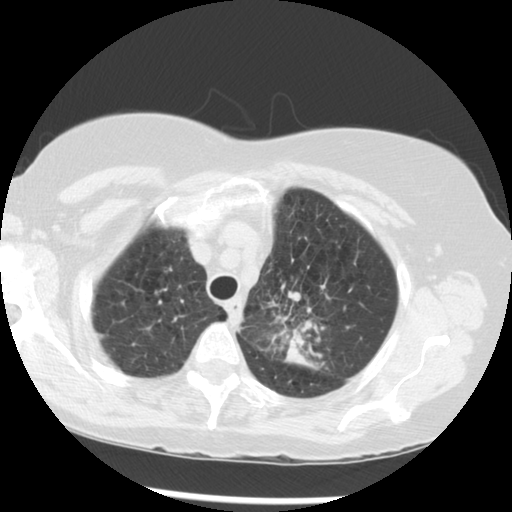
Axial slice from a low-dose chest CT screening exam. Third screening round (two years after baseline). Lung window (W 1500 / L -600 HU). 2.5 mm slice thickness. Standard (soft-tissue) reconstruction kernel (STANDARD). Slice 231 of 283 in the series. 512 × 512 image matrix. Female participant, aged 70 years at enrolment. Current smoker at enrolment.
• Lesion marked by an expert reader, bounding box <255,281,352,369> (left, top, right, bottom; pixels).
• The exam's reader record, not a measurement of the box and not confirmed to be the same lesion: non-calcified nodule or mass ≥4 mm, left upper lobe, 32 × 26 mm, spiculated (stellate) margins, soft tissue attenuation, pre-existing on the prior screen: yes; interval growth: yes.